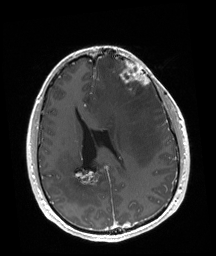
Brain MRI from a brain-tumour surgery series, one axial slice; slice 73 of 192 in the series (ordered by position); T1-weighted post-contrast; 1 mm slice thickness; 216 × 256 image matrix, field of view 219 × 260 mm.
Outlined on this slice (expert manual segmentation):
- tumour: box from (x=120, y=61) to (x=149, y=94) px